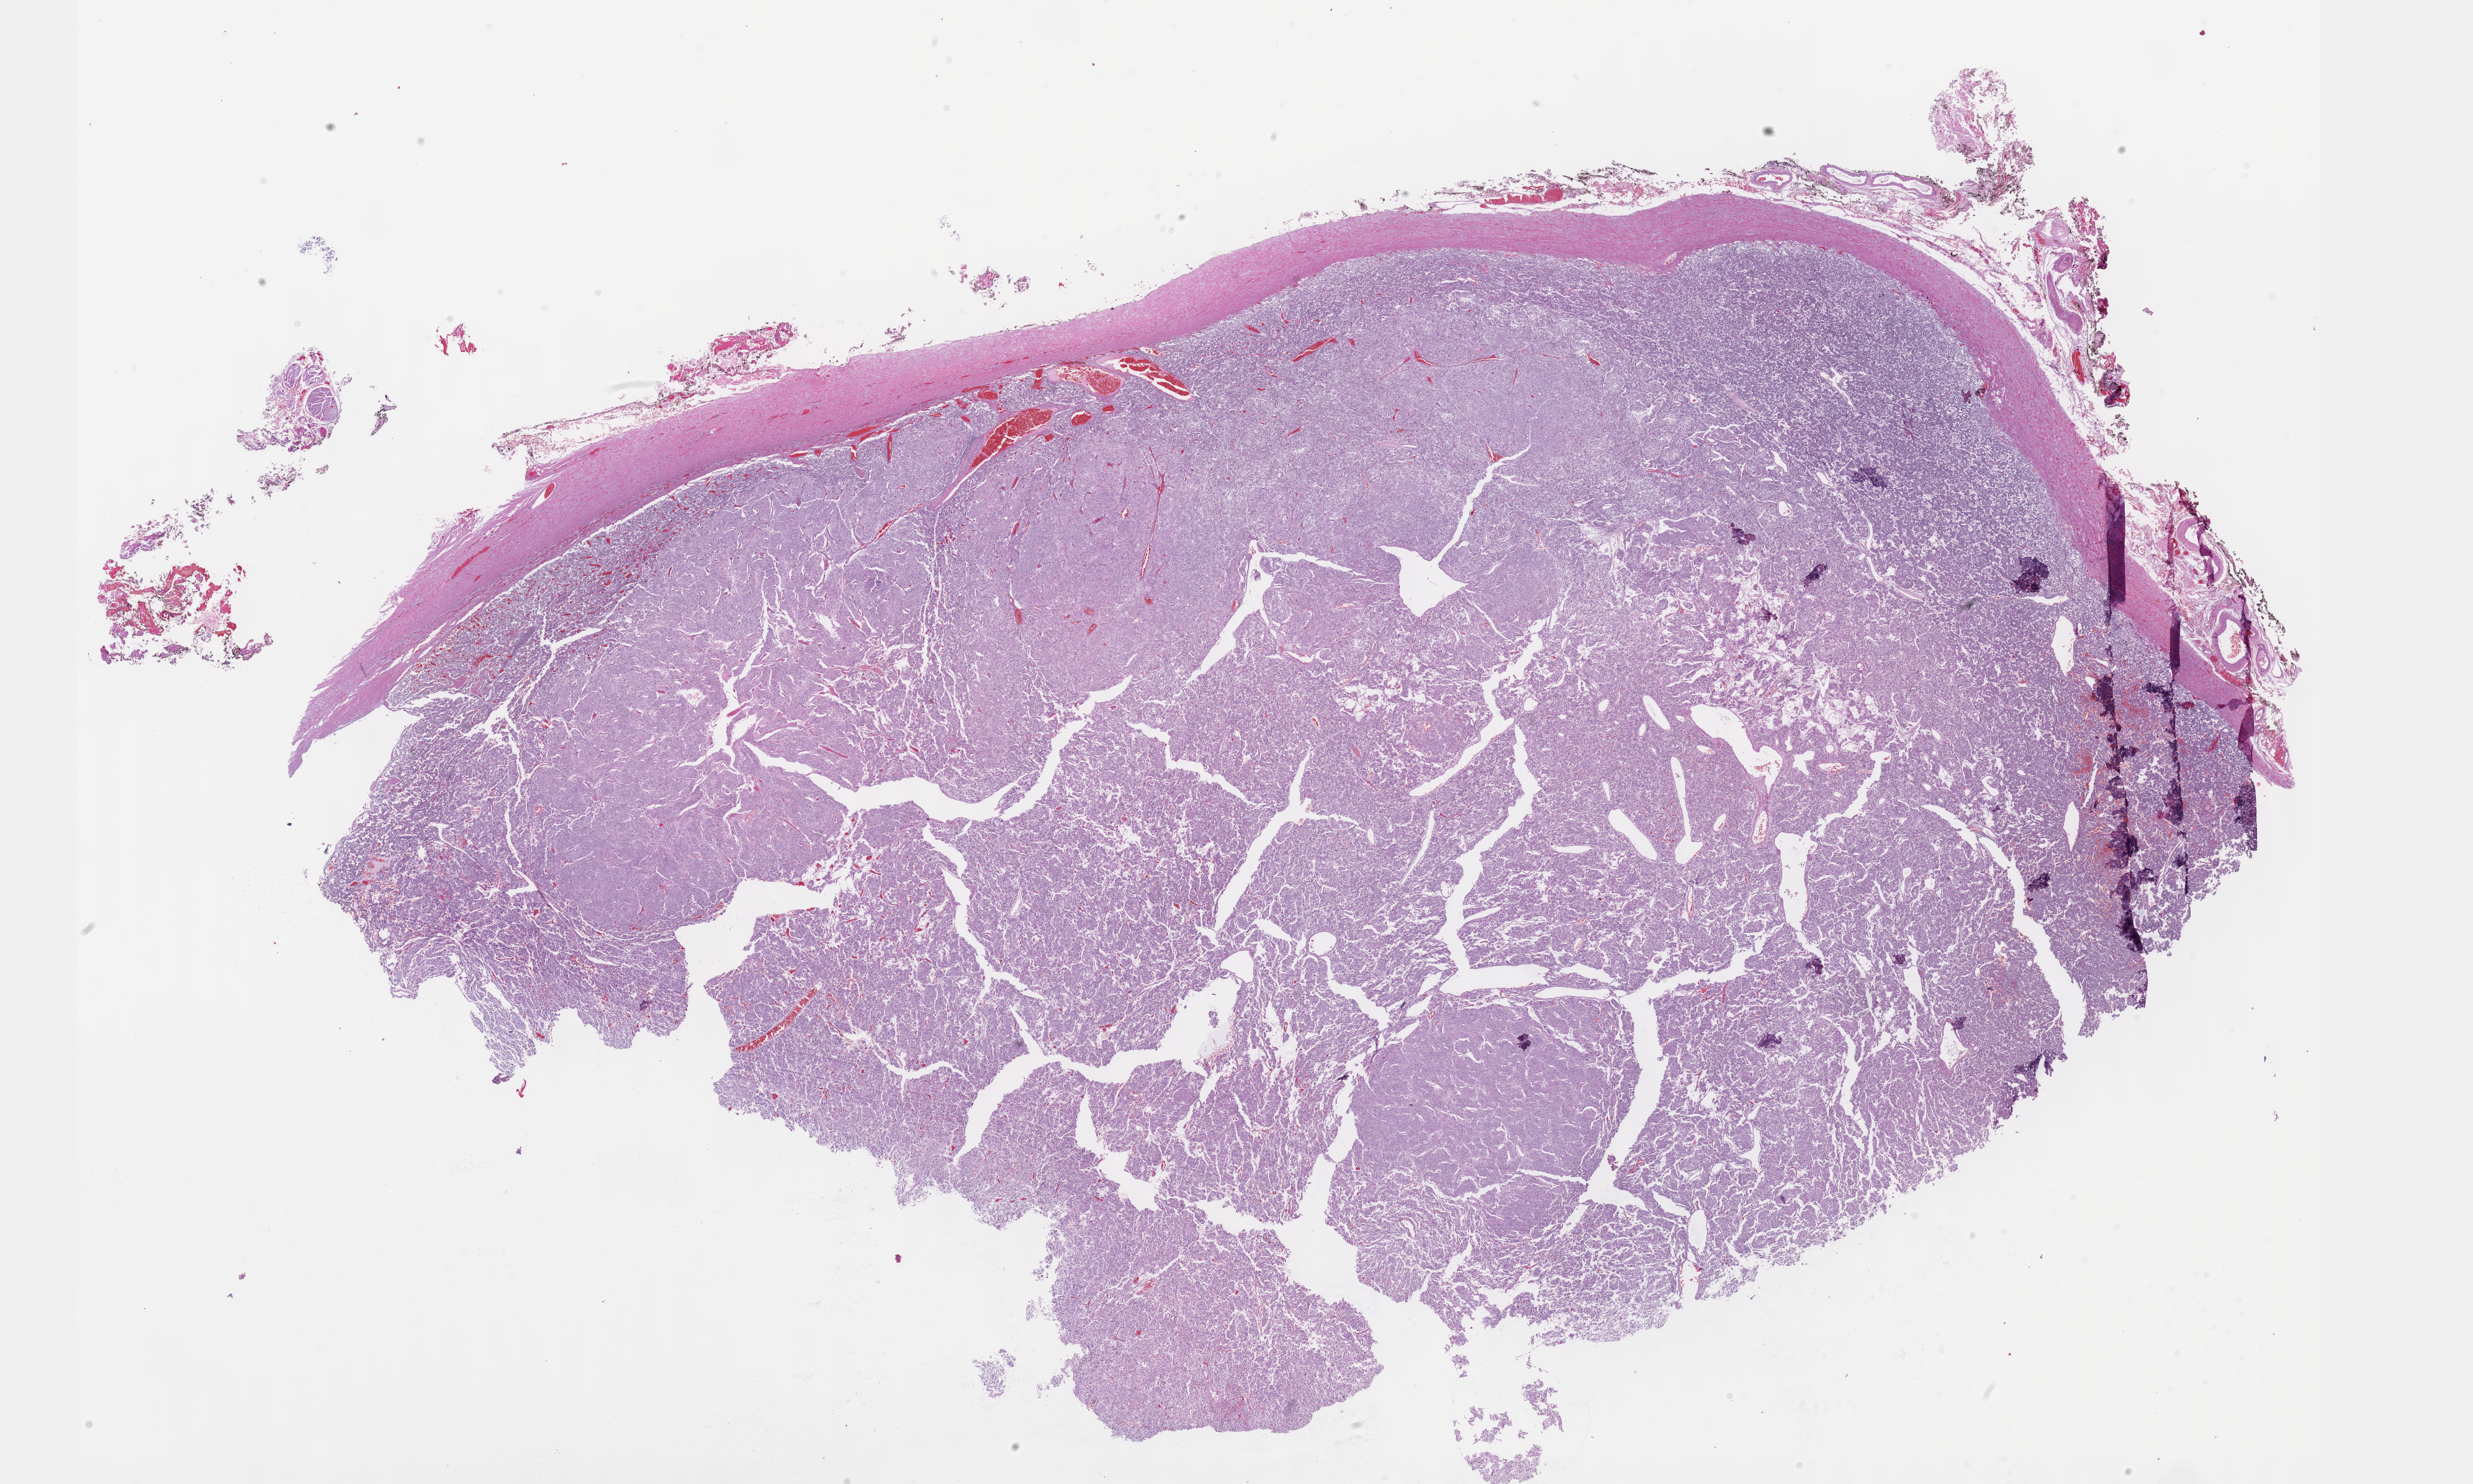
Whole-slide histology image, Hematoxylin and eosin (H&E) stained — a low-resolution overview of the entire scanned area, about 32.2 x 19.3 mm (acquisition: 40x scan), formalin-fixed paraffin-embedded (FFPE) diagnostic section, sample: primary tumour, adrenal gland. Female, age 44 years at initial diagnosis.
Histologic diagnosis: Pheochromocytoma, NOS. Laterality: right.